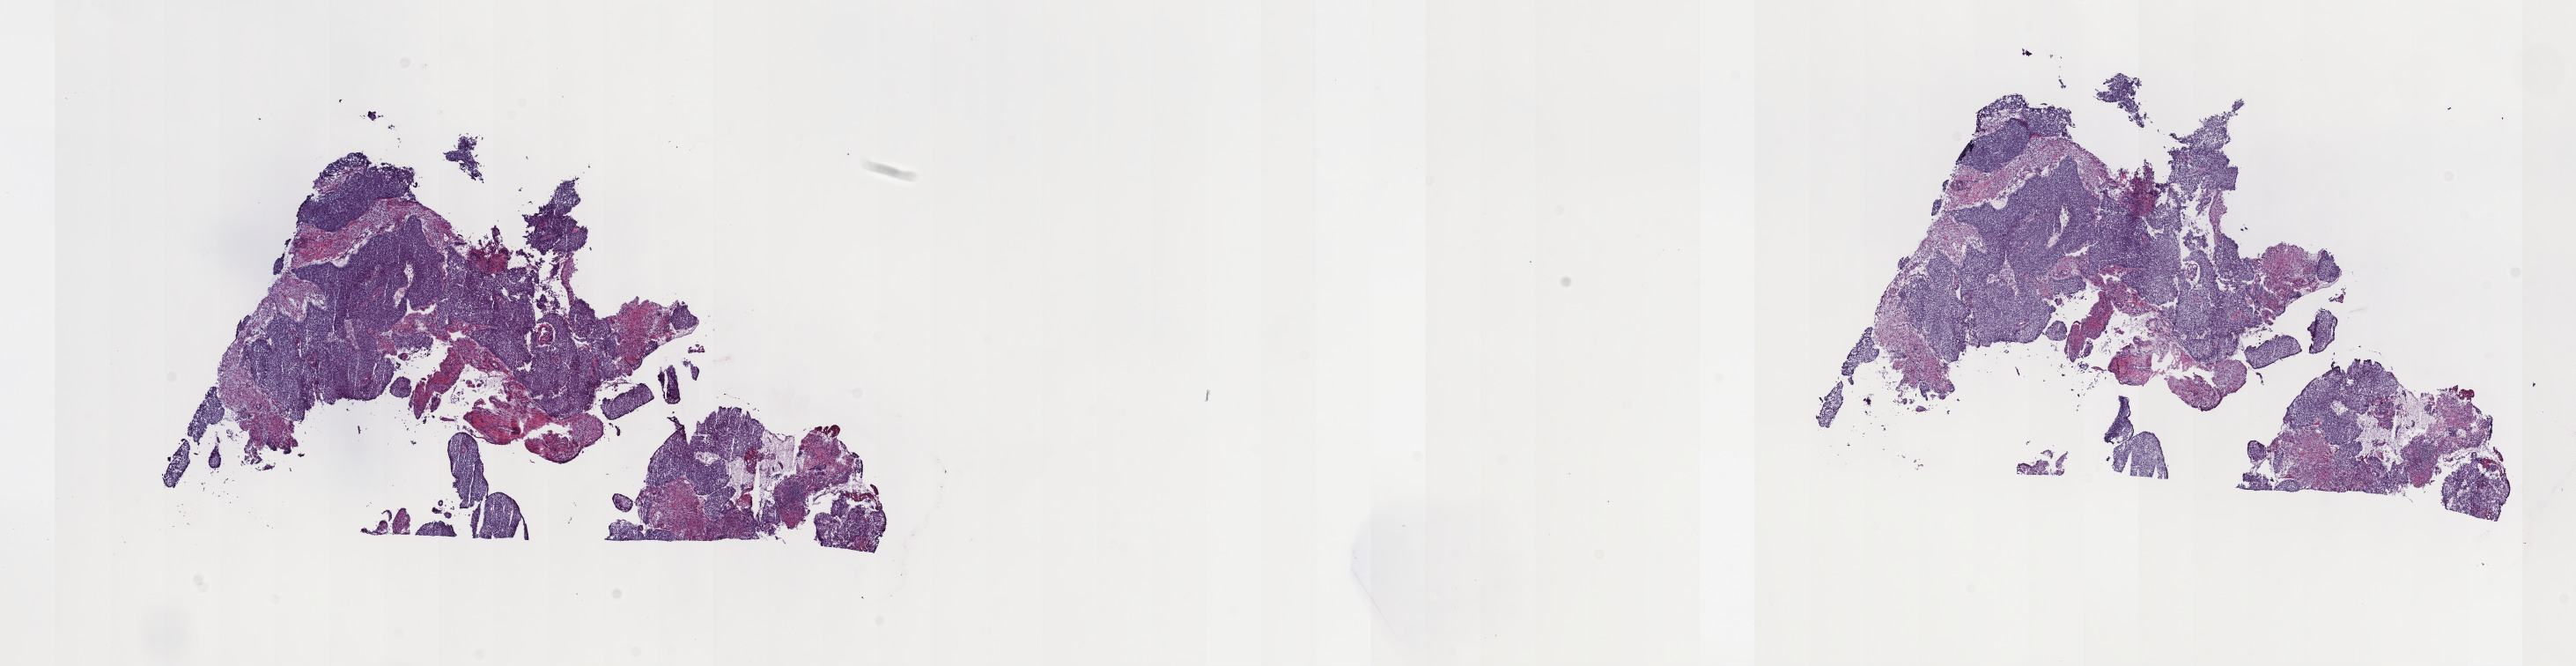
Digitized Hematoxylin and eosin (H&E) stained tissue section (whole slide), shown as a low-resolution overview of the whole scanned area (about 23.7 x 6.1 mm, slide scanned at 40x); frozen section; primary tumour sample from the cervix. Patient: female, age at initial diagnosis 74 years. Pathologist review of this section (percent, as recorded): tumour cells 70%, tumour nuclei 70%, normal cells 15%, stromal cells 15%, necrosis 0%. Infiltration values recorded for this section: lymphocyte infiltration 5%, monocyte infiltration 0%, neutrophil infiltration 0%.
Pathologic diagnosis: Squamous cell carcinoma, NOS (cervix uteri). FIGO stage: IB.